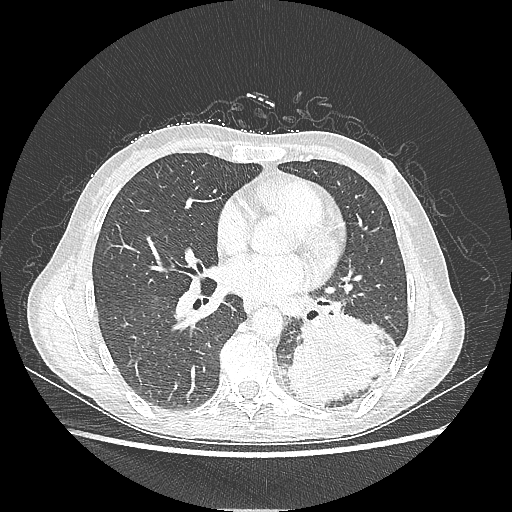
Chest CT, one axial slice; reconstruction kernel LUNG; lung window (W 1500 / L -600 HU); 1.25 mm slice thickness; 512 × 512 image matrix. Patient: female, 53 years. From the clinical record (not read from this slice): clinical TNM (as recorded): T3 N0 M0.
Outlined on this slice (rectangle marked by the reading radiologist):
- lung tumour (recorded histology: adenocarcinoma): bounding box [x1, y1, x2, y2] px = [287, 314, 396, 407]